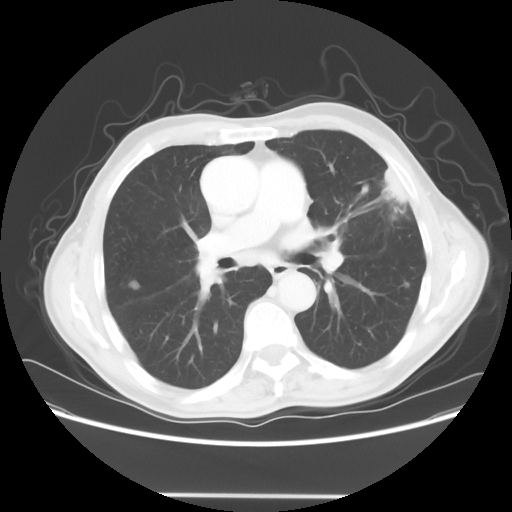
Chest CT, one axial slice. Position 36 of 64 along the scan axis. 120 kVp. Lung window (W 1500 / L -600 HU). 5 mm slice thickness. 512 × 512 image matrix, field of view 392 × 392 mm. Patient: male, 71 years. From the clinical record (not read from this slice): clinical TNM (as recorded): T1c N0 M0.
Outlined on this slice (bounding box drawn by a radiologist):
- lung tumour (recorded histology: adenocarcinoma): bounding box (x1, y1, x2, y2) in pixels: (378, 161, 413, 213)